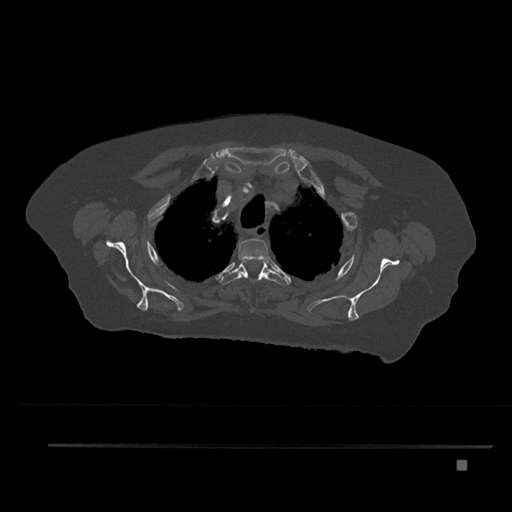
CT including the spine, one axial slice; slice 648 of 797 in the series (ordered by position); reconstruction kernel Br40s/3; 120 kVp; bone window (W 1800 / L 400 HU); 0.5 mm slice thickness; 512 × 512 image matrix, field of view 437 × 437 mm. Female patient, age 76 years. Case-level facts recorded for this patient, not image findings: primary cancer: lung; vertebrae with lytic lesions (as recorded): T11, L3.
Outlined on this slice (semi-automatic segmentation, software-assisted and operator-edited):
- T2 vertebra: bounding box <238,238,271,271> (left, top, right, bottom; pixels)
- T3 vertebra: <219,260,289,286>